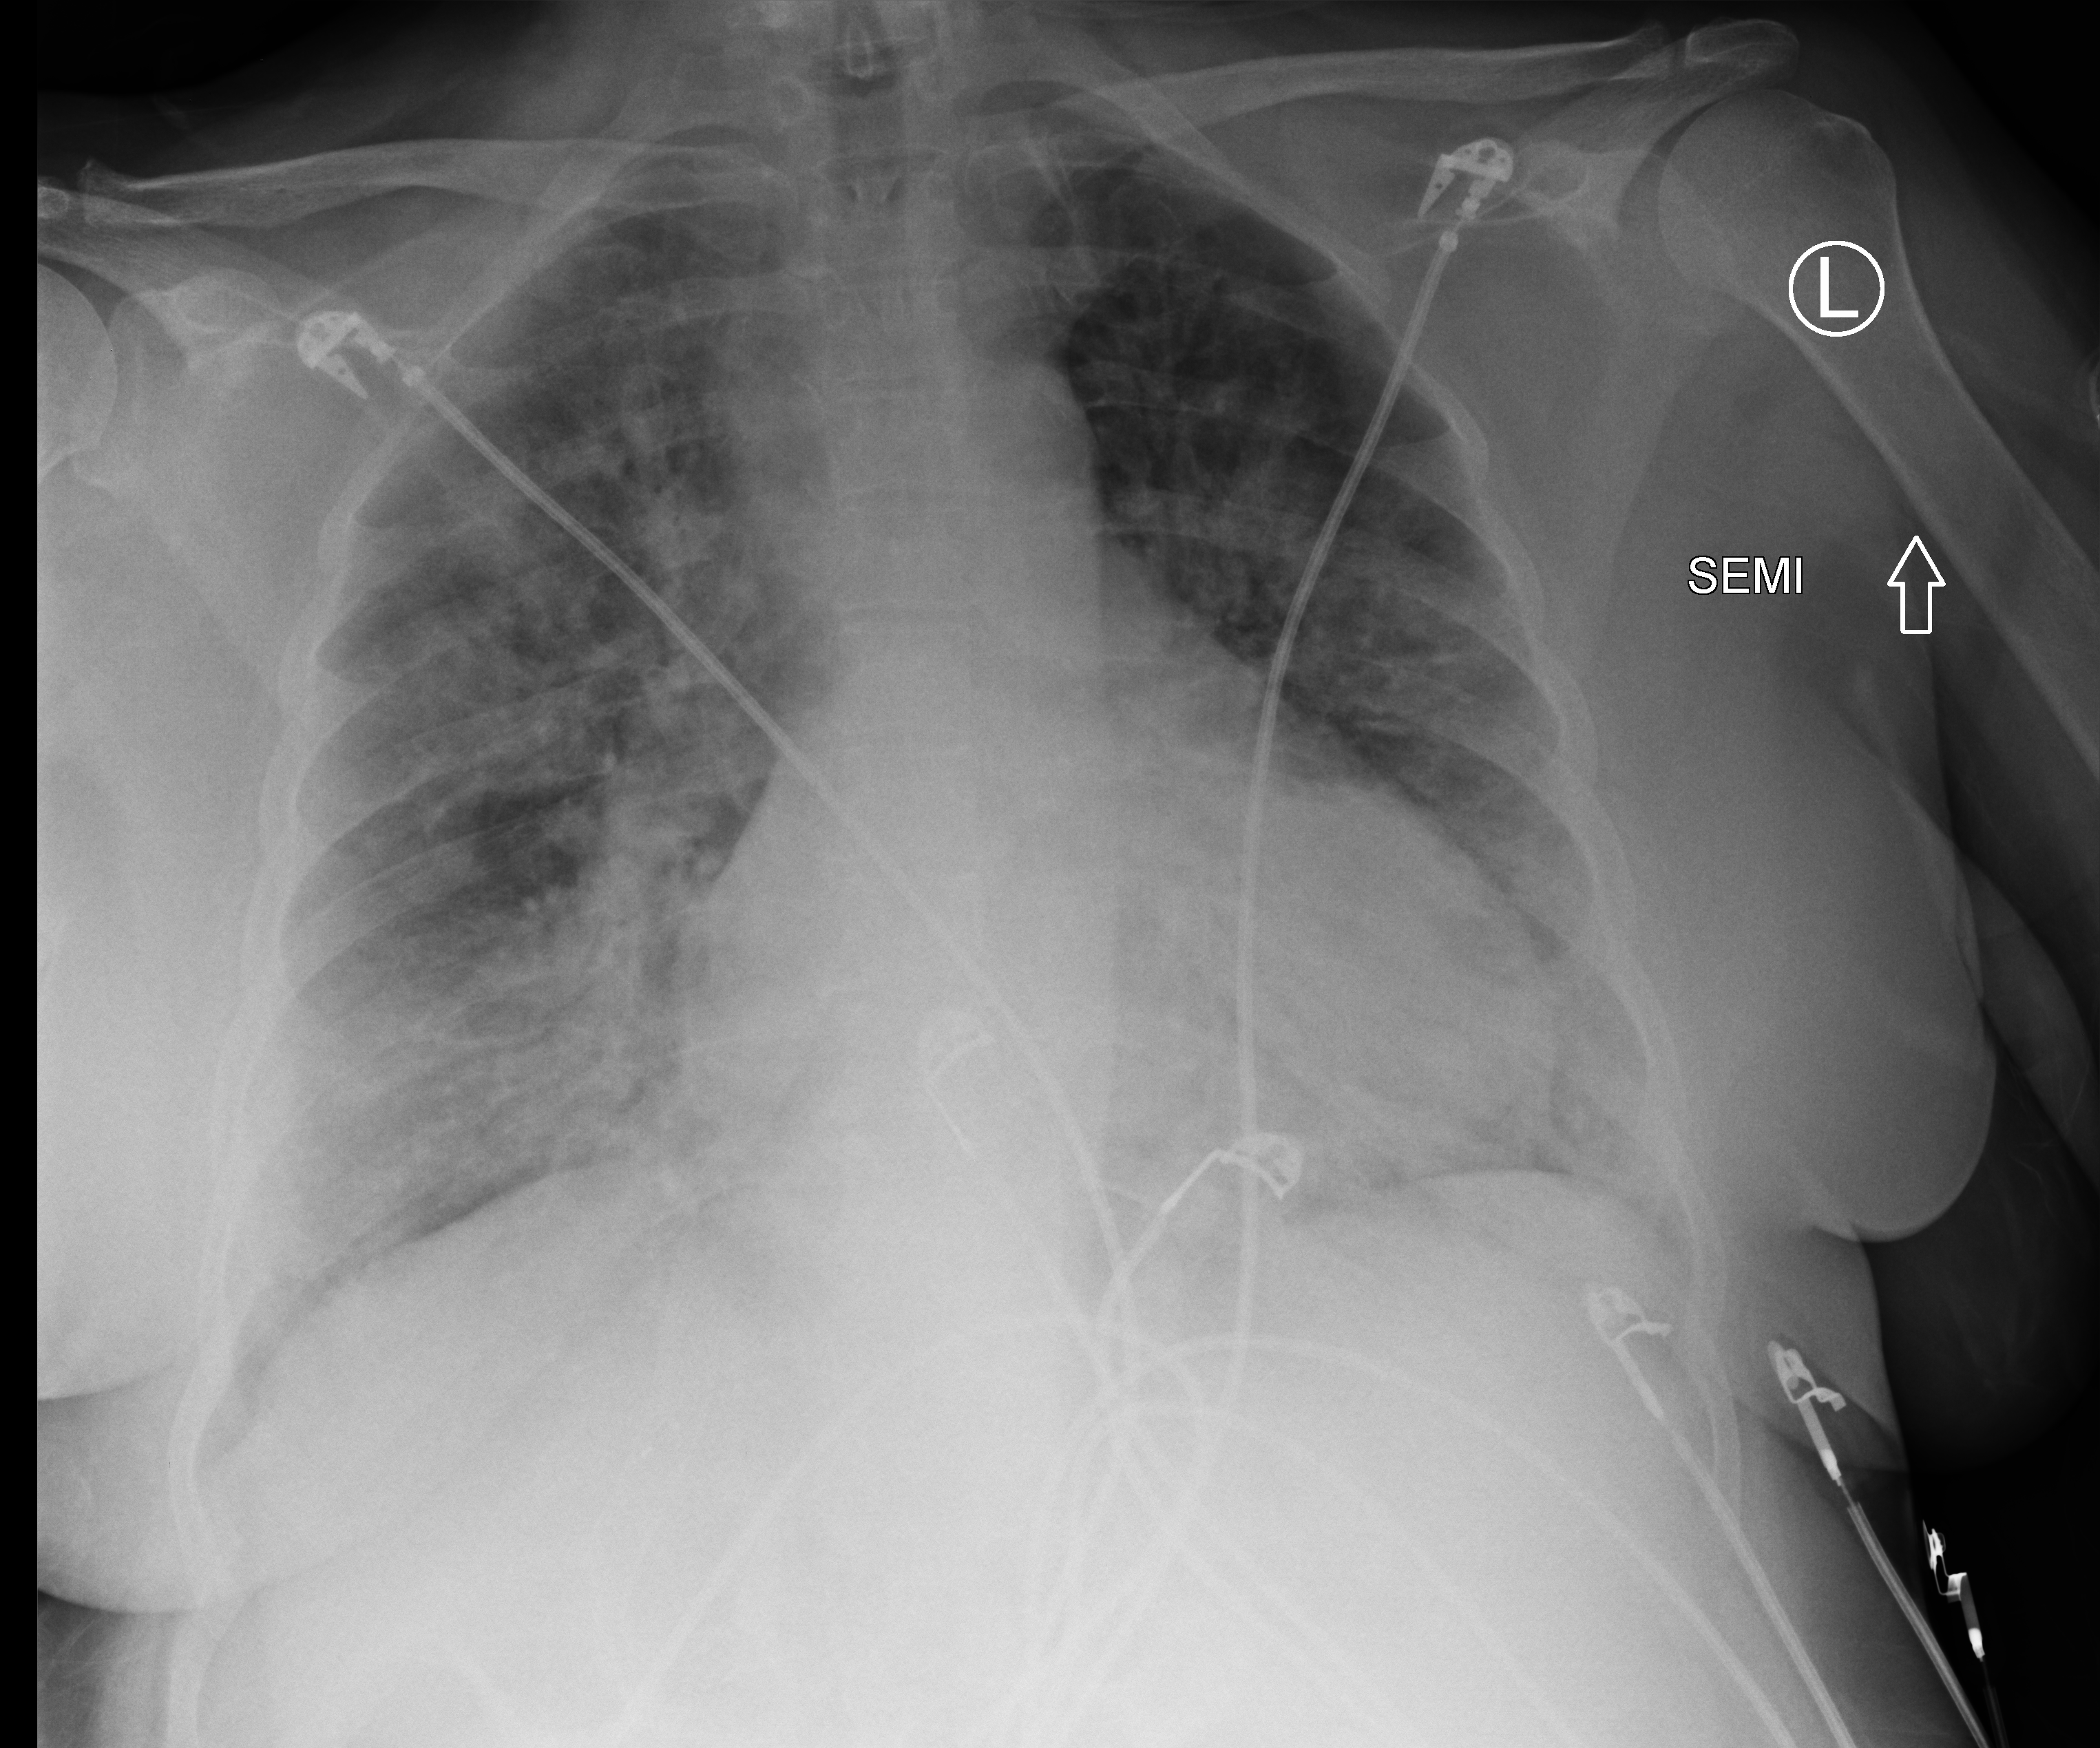
Portable chest radiograph, anteroposterior (AP) projection. Female patient hospitalised with COVID-19, age 60–74 years.
Hospital-stay facts (about this admission, not read from this image; timing relative to this image not recorded):
- diabetes (admission record): yes
- length of hospital stay: 17 days
- COPD (admission record): no